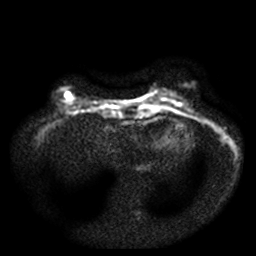
Breast MRI, one axial slice; position 12 of 49 along the scan axis; diffusion-weighted series; image 2 of 4 stored at this slice position (different b-values; order by instance number); 3 T; 5 mm slice thickness; 256 × 256 image matrix, field of view 340 × 340 mm. Female patient.
Structures marked on this image (expert manual segmentation):
- tumour on diffusion-weighted imaging: bounding box [x1, y1, x2, y2] px = [66, 92, 71, 99]